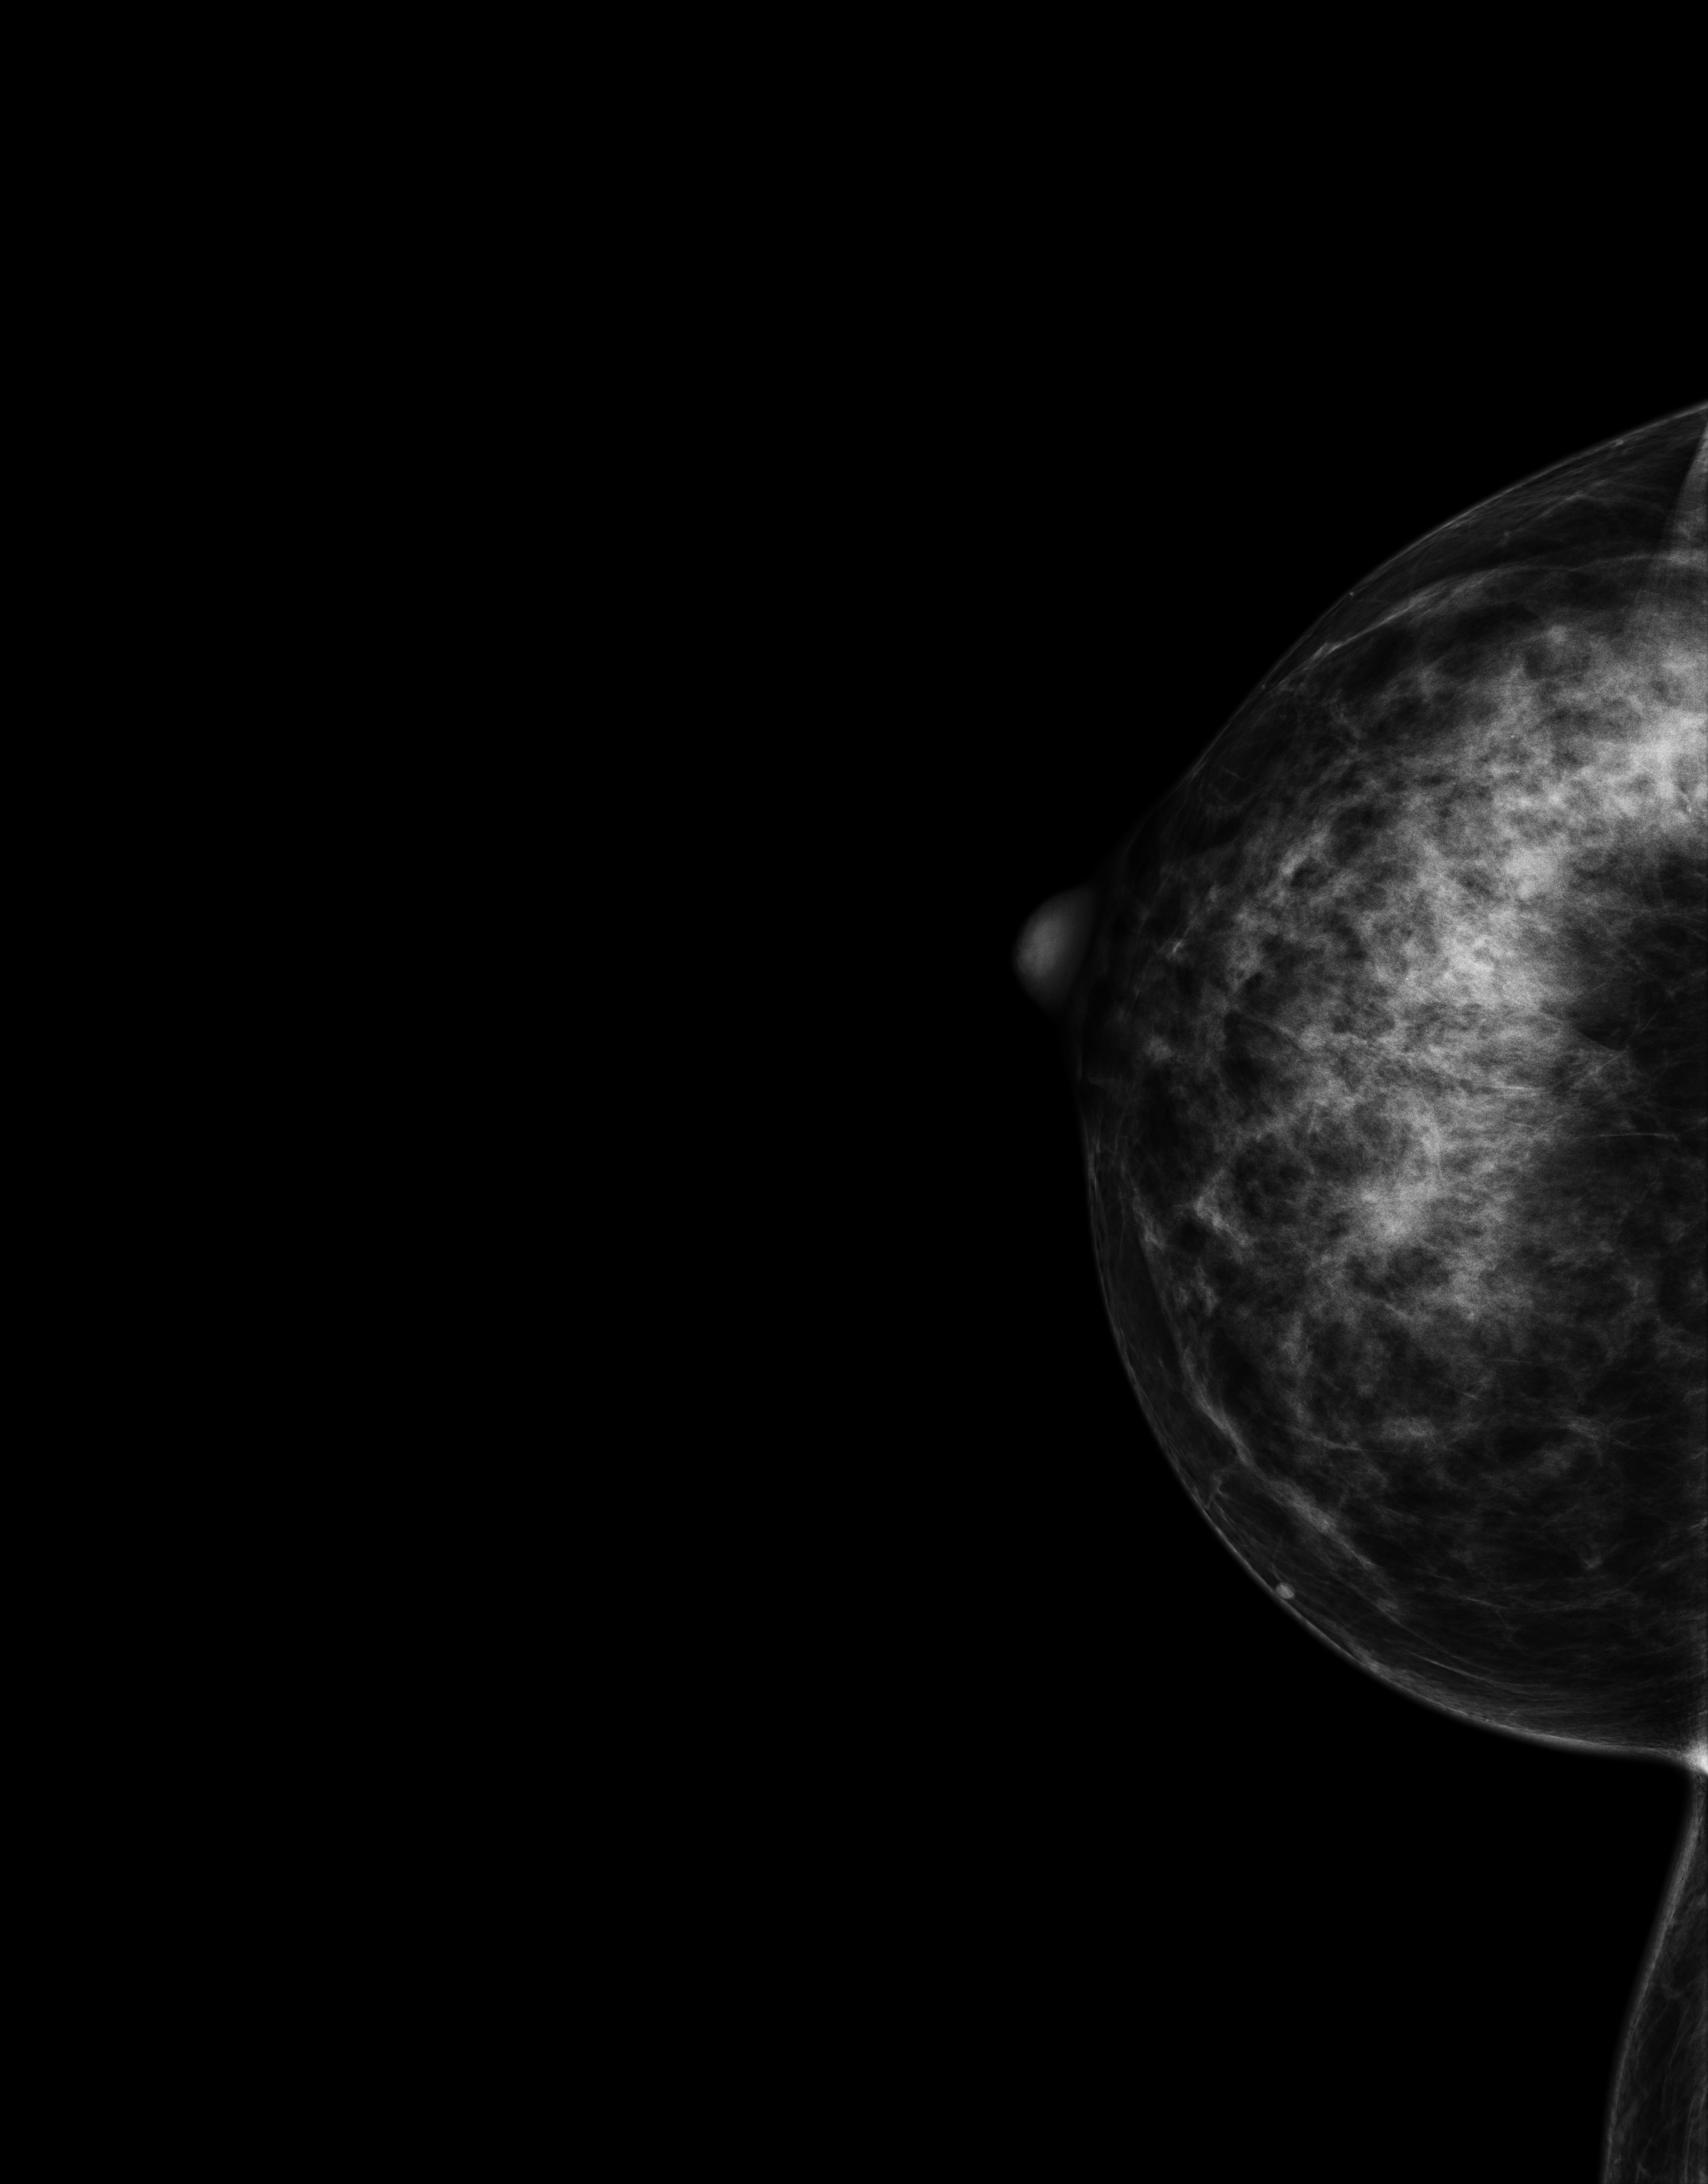
Screening examination; compressed breast thickness 69 mm; system: Senographe Essential ADS_56.21.3. Patient aged 42 years (female).
Image type: full-field digital mammogram. Breast: right. Projection: craniocaudal (CC) view.